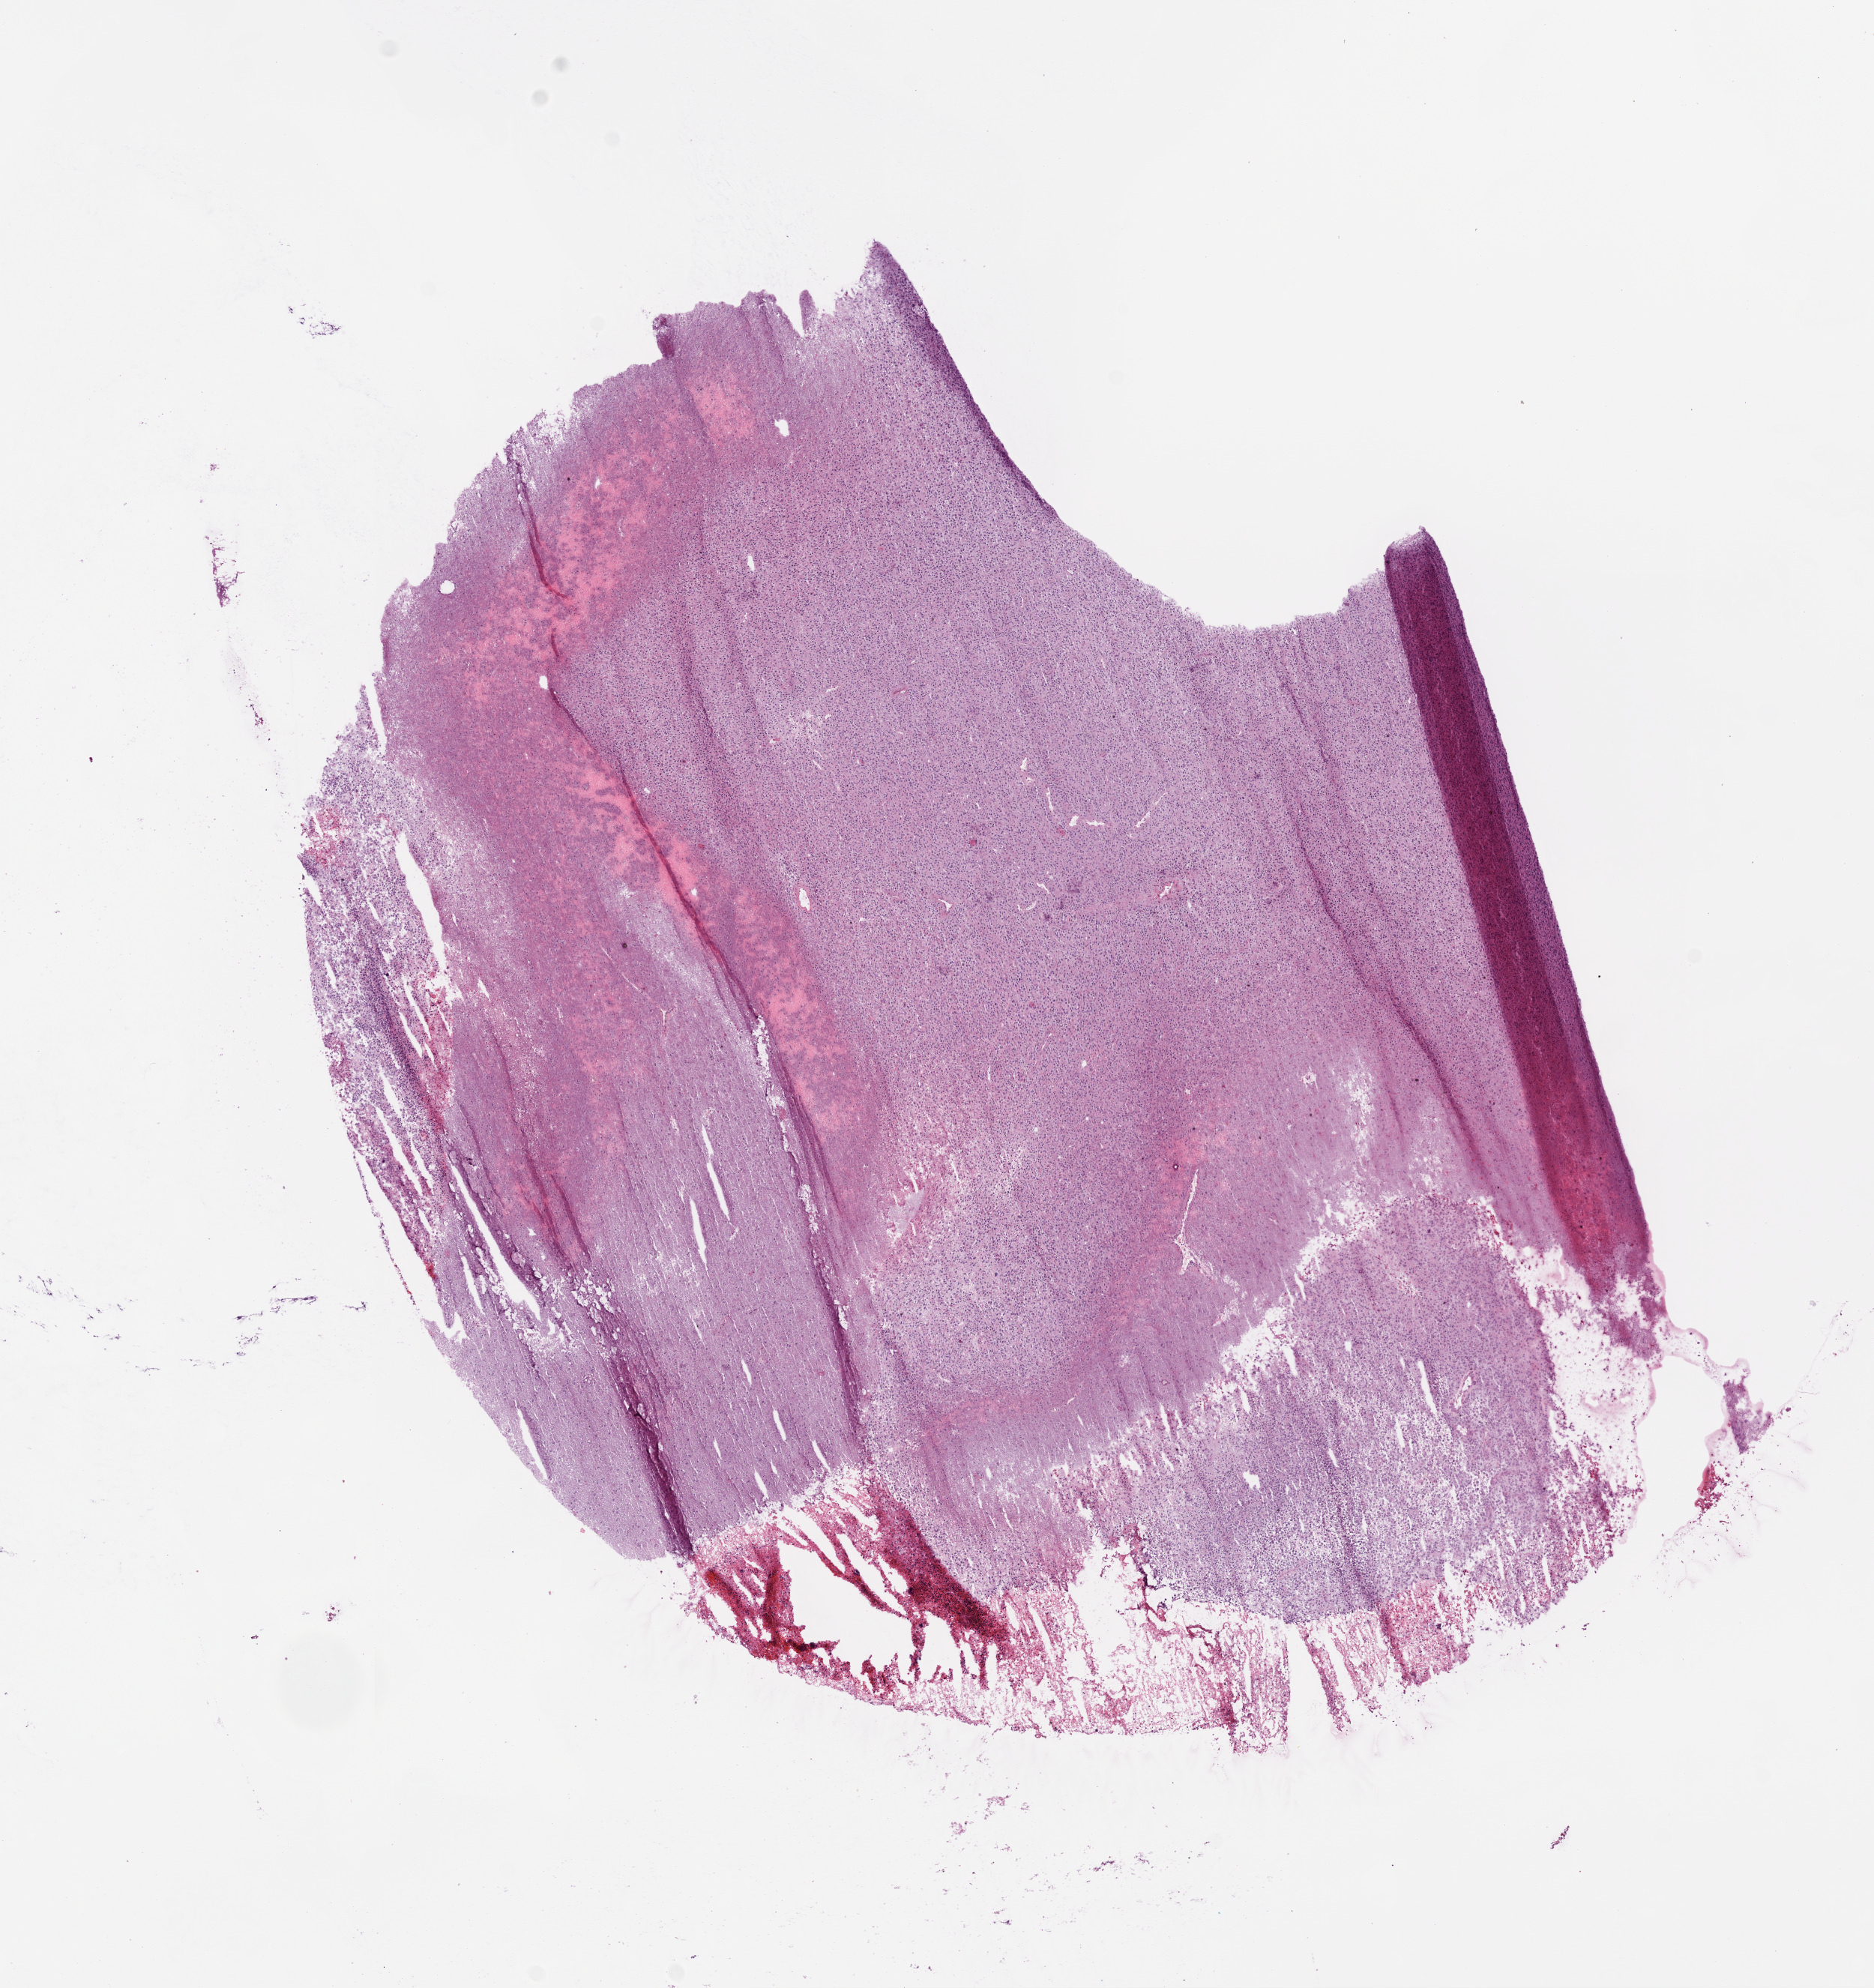
H&E whole-slide image — whole scanned area (about 10.0 x 10.6 mm) shown as a low-resolution overview, frozen section from the bottom of the tissue portion, brain, primary tumour sample. Female patient; age at initial diagnosis 23 years. Pathologist review of this section (percent, as recorded): tumour cells 85%, tumour nuclei 80%, normal cells 0%, stromal cells 0%, necrosis 15%.
Pathologic diagnosis: Glioblastoma.